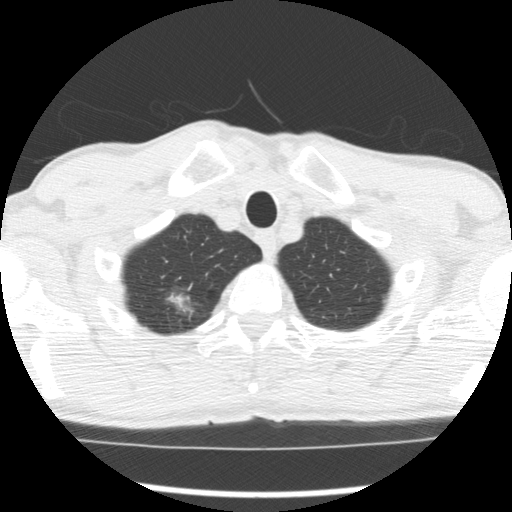
Axial slice from a low-dose chest CT screening exam, first (baseline) screen, lung window (W 1500 / L -600 HU), 2.5 mm slice thickness, slice 24 of 277 in the series, 512 × 512 image matrix, field of view 320 × 320 mm. Male, age 66 years at enrolment. Former smoker at enrolment.
Expert reader's lesion annotation, bounding box <151,283,203,331> (left, top, right, bottom; pixels). The screening reader recorded 4 non-calcified nodules or masses ≥4 mm on this exam (right upper lobe, right upper lobe, right upper lobe, left lower lobe); which of them this box marks is not recorded. Official screen result: positive, change unspecified: nodule(s) >= 4 mm or enlarging nodule(s), mass(es), or other non-specific abnormalities suspicious for lung cancer.